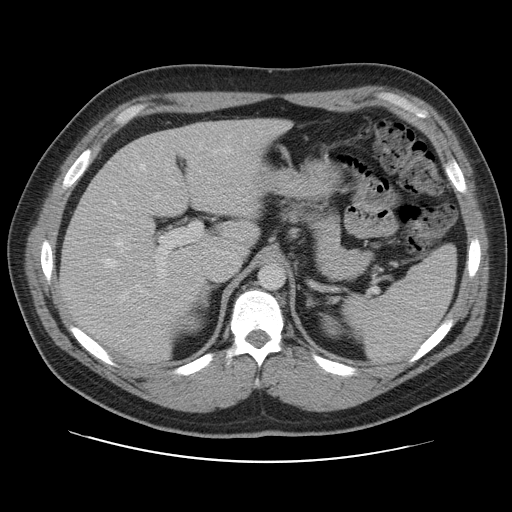
Contrast-enhanced abdominal CT, one axial slice. Position 74 of 109 along the scan axis. 120 kVp. Intravenous contrast given. Soft-tissue window (W 400 / L 40 HU). 5 mm slice thickness. 512 × 512 image matrix, field of view 402 × 402 mm. Male patient, age 35 years. Case-level facts recorded for this patient, not image findings: diagnosis: colorectal cancer liver metastases, imaged before liver resection; multiple liver metastases: yes; largest metastasis: 2.8 cm; chemotherapy before resection: yes.
Annotated regions visible in this slice (manually delineated by an expert):
- hepatic veins: bounding box (x1, y1, x2, y2) in pixels: (101, 146, 232, 300)
- liver: (61, 119, 287, 361)
- planned liver remnant (the part of the liver to remain after resection): (61, 119, 281, 359)
- portal vein (with intrahepatic branches): (117, 160, 202, 298)